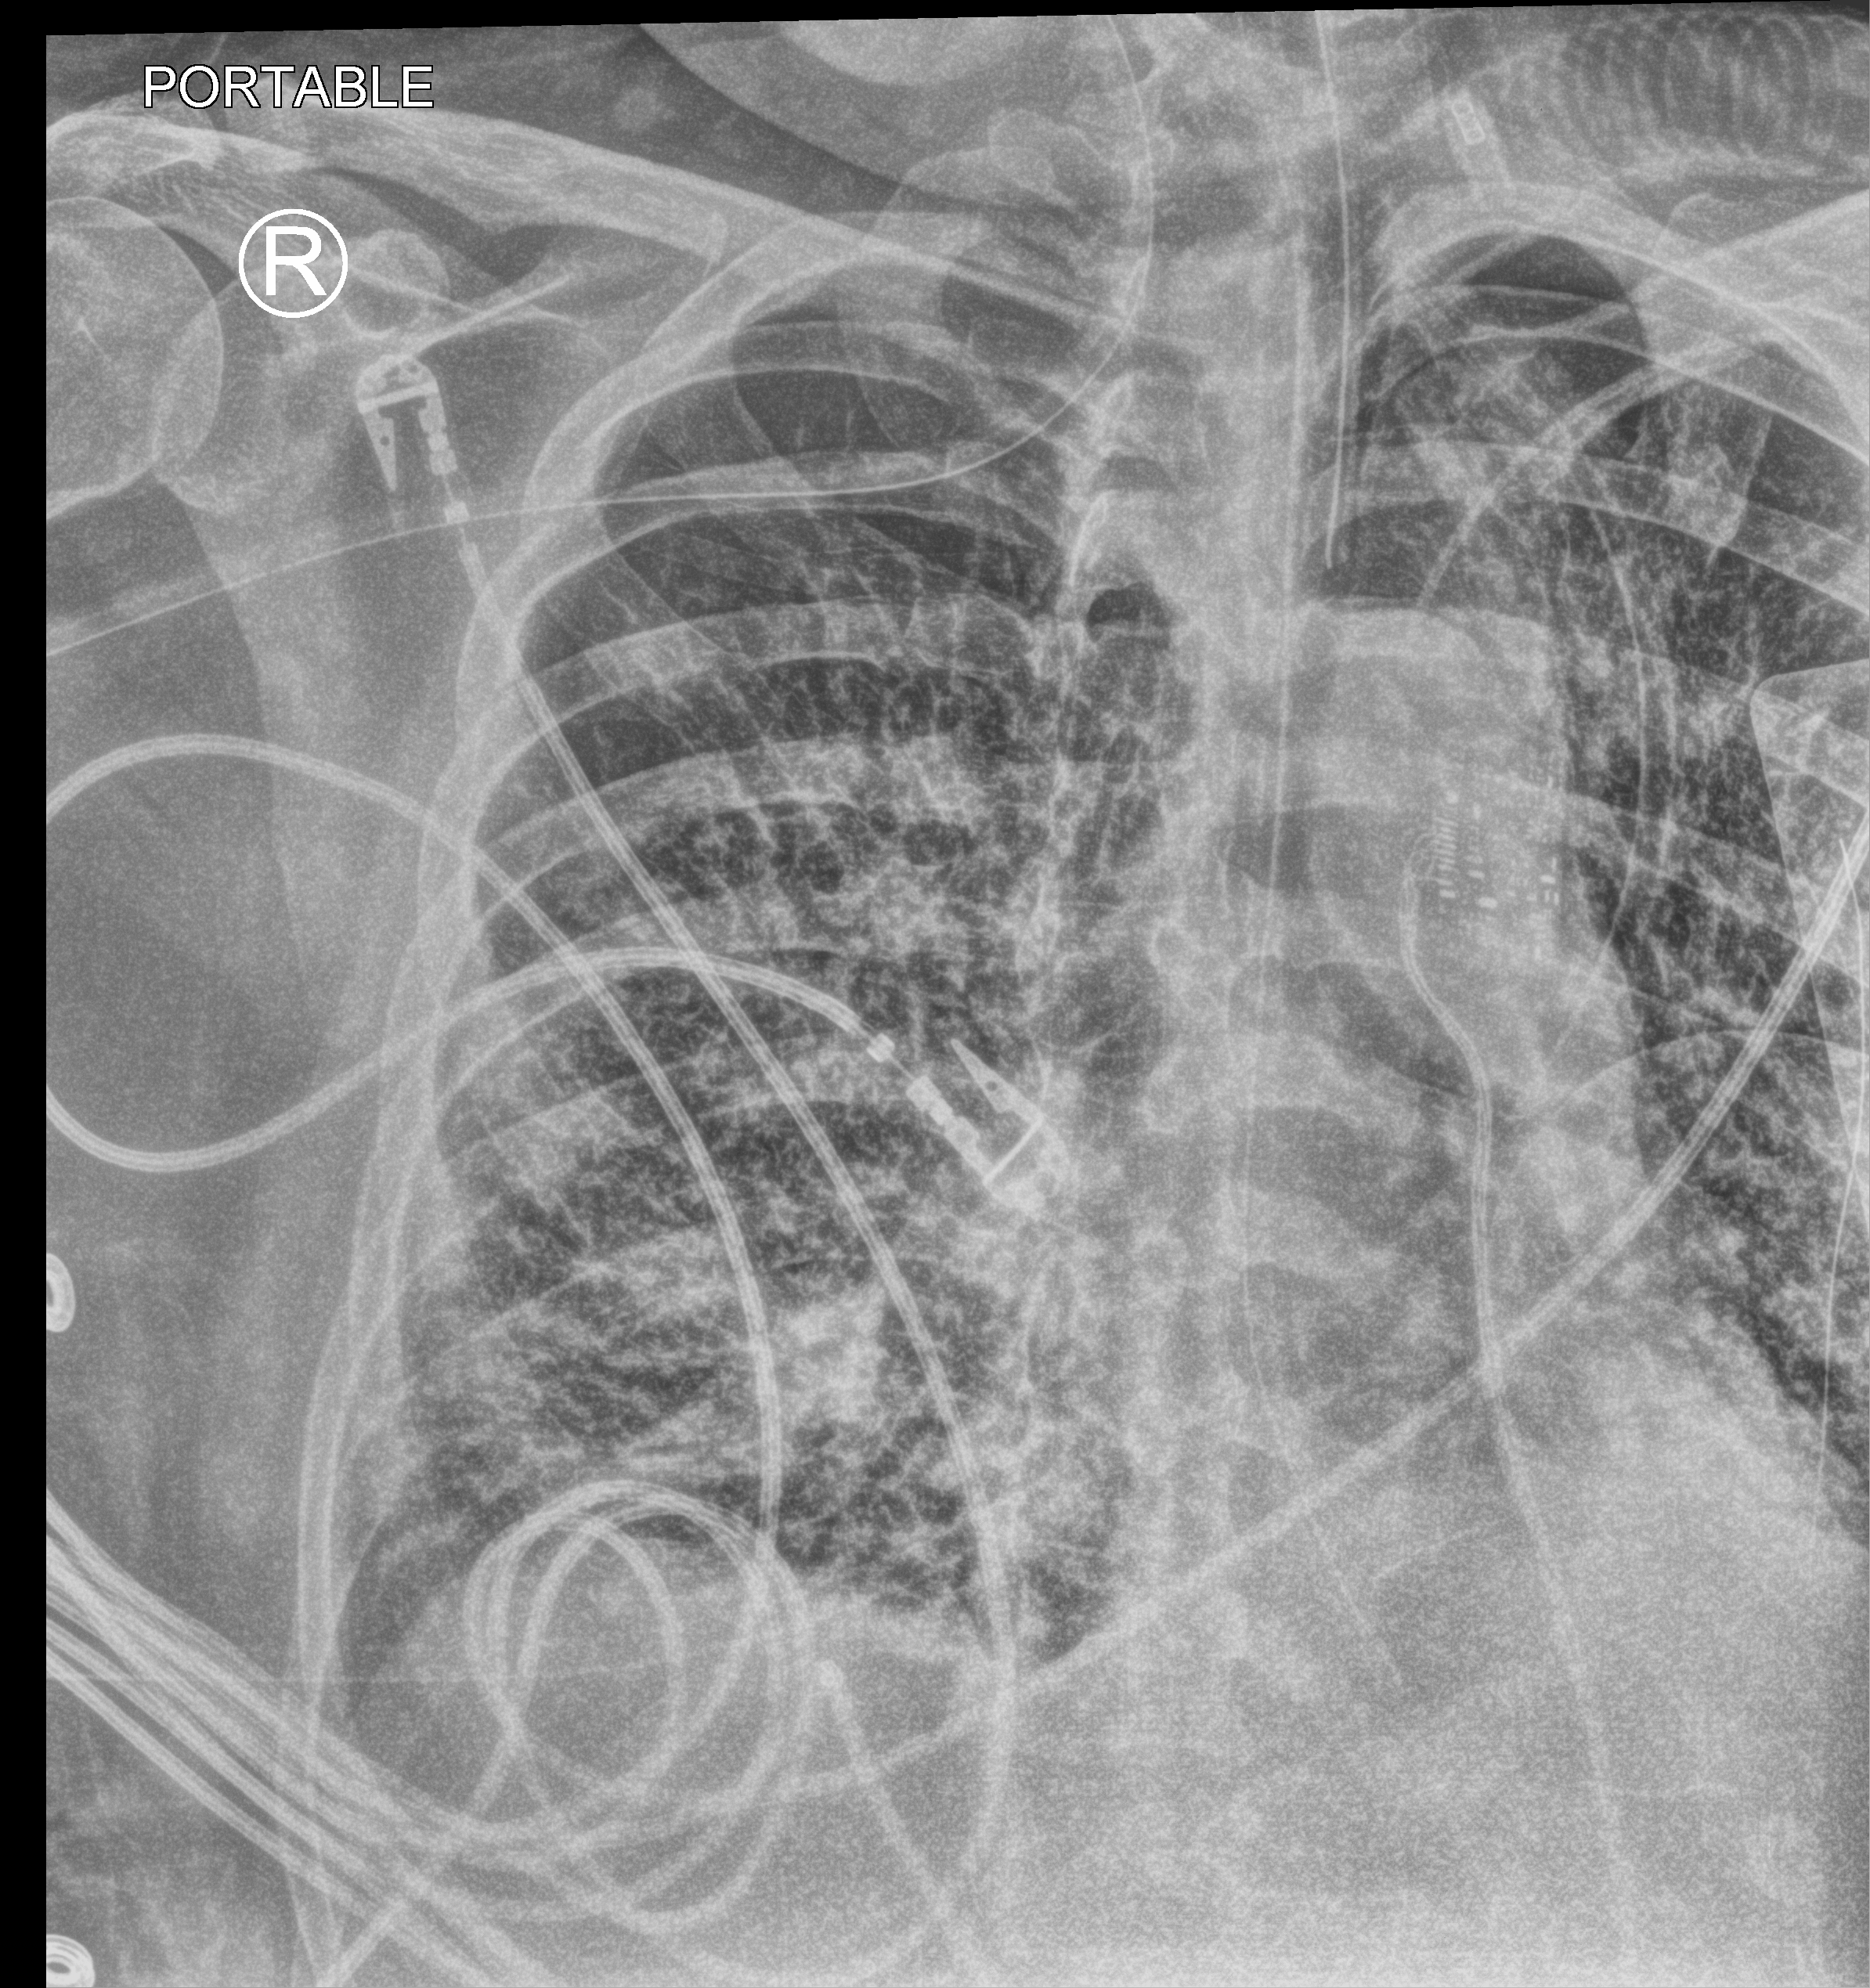
Chest X-ray (portable); anteroposterior (AP) projection. Adult patient hospitalised with COVID-19, age 18–59 years.
From the hospital-stay record, not from the radiograph (when in the stay this image was taken is not recorded): hypertension (admission record): no; admitted to intensive care during this hospital stay: yes.